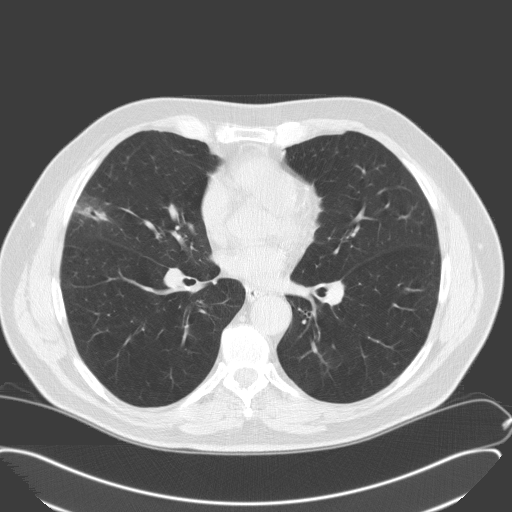
Low-dose screening chest CT, axial slice, second annual screen, lung window (W 1500 / L -600 HU), slice 89 of 175 in the series, 512 × 512 image matrix, field of view 400 × 400 mm. Male participant, aged 65 years at enrolment.
• Expert reader's lesion annotation, bounding box [x1, y1, x2, y2] px = [53, 191, 116, 244].
• Screening reader's record for this exam: no non-calcified nodule ≥4 mm recorded.
• Later outcome: lung cancer diagnosed 346 days after this screen (after the third annual screen) — adenocarcinoma, NOS, right middle lobe, moderately differentiated (G2), stage IA (AJCC 6th edition), 25 mm at pathology.